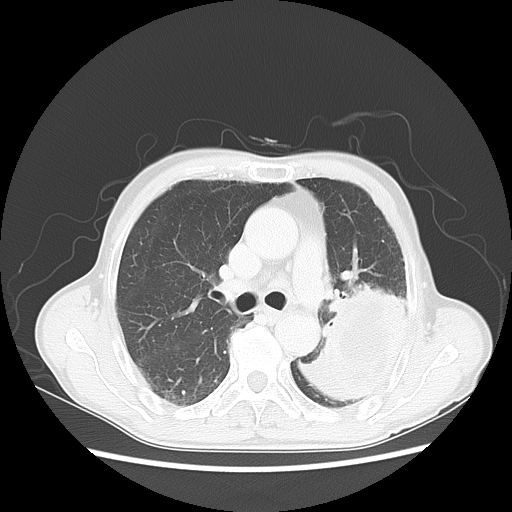
Chest CT, one axial slice. Position 33 of 51 along the scan axis. Reconstruction kernel LUNG. 120 kVp. Lung window (W 1500 / L -600 HU). 5 mm slice thickness. 512 × 512 image matrix. Patient: male, 64 years. From the clinical record (not read from this slice): clinical TNM (as recorded): T4 N0 M0.
Outlined on this slice (rectangle marked by the reading radiologist):
- lung tumour (recorded histology: squamous cell carcinoma): bounding box [x1, y1, x2, y2] px = [307, 284, 401, 411]